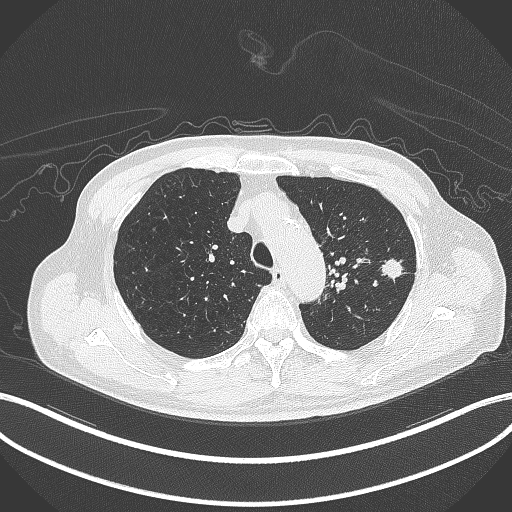
Chest CT, one axial slice; position 339 of 417 along the scan axis; reconstruction kernel B70f; 120 kVp; lung window (W 1500 / L -600 HU); 1 mm slice thickness; 512 × 512 image matrix, field of view 400 × 400 mm. Male patient, age 77 years. From the clinical record (not read from this slice): clinical TNM (as recorded): T3 N1 M0.
Outlined on this slice (bounding box drawn by a radiologist):
- lung tumour (recorded histology: adenocarcinoma): bounding box [x1, y1, x2, y2] px = [379, 251, 405, 283]